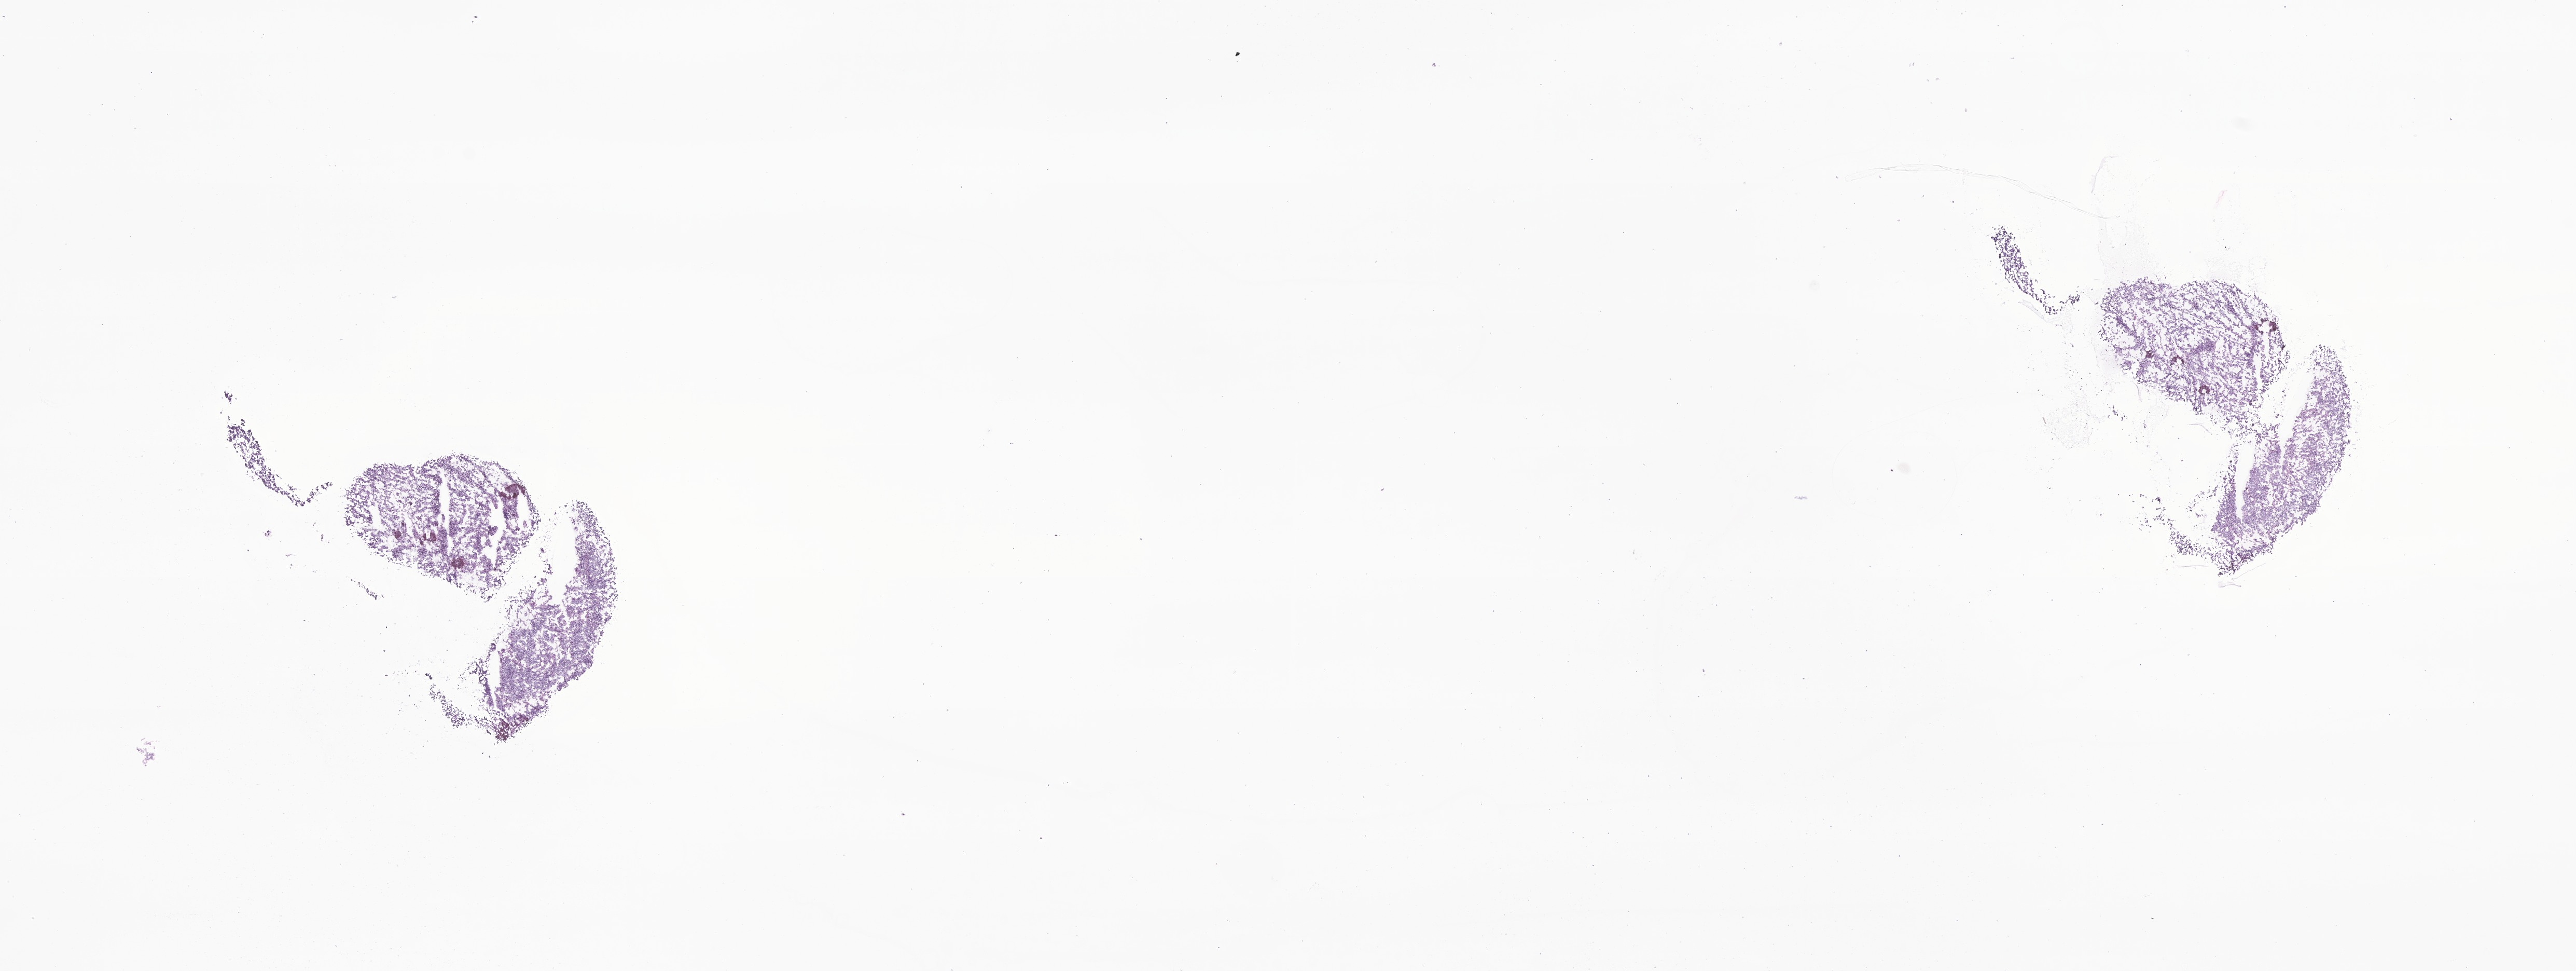
Whole-slide image, haematoxylin and eosin stain of tumor tissue from the eye — shown as a low-resolution overview of the whole scanned area (about 20.9 x 7.9 mm). Frozen section. Patient male; age 344 days.
Diagnosis (ICD-O-3 morphology term): Retinoblastoma, NOS.